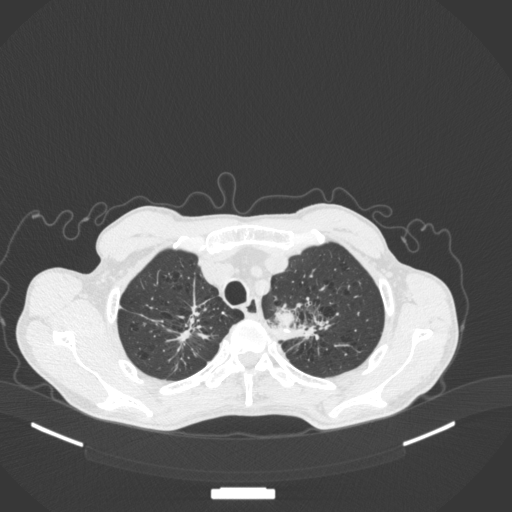
Chest CT, one axial slice. Slice 363 of 394 in the series (ordered by position). Lung window (W 1500 / L -600 HU). 1 mm slice thickness. 512 × 512 image matrix, field of view 400 × 400 mm. Male patient, age 65 years. From the clinical record (not read from this slice): clinical TNM (as recorded): T2b N0 M0; histopathological grade: G2.
Annotated regions visible in this slice (rectangle marked by the reading radiologist):
- lung tumour (recorded histology: adenocarcinoma): bounding box [x1, y1, x2, y2] px = [270, 296, 300, 336]